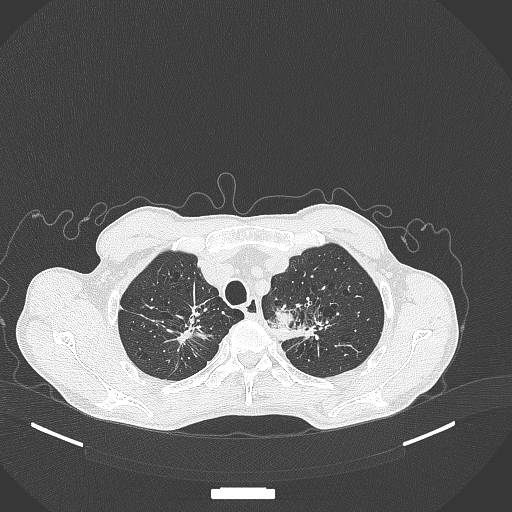
Chest CT, one axial slice. Position 364 of 386 along the scan axis. 120 kVp. Lung window (W 1500 / L -600 HU). 512 × 512 image matrix. Male patient, age 65 years. Case-level facts recorded for this patient, not image findings: clinical TNM (as recorded): T2b N0 M0; histopathological grade: G2.
Outlined on this slice (rectangle marked by the reading radiologist):
- lung tumour (recorded histology: adenocarcinoma): bounding box [x1, y1, x2, y2] px = [272, 301, 298, 330]